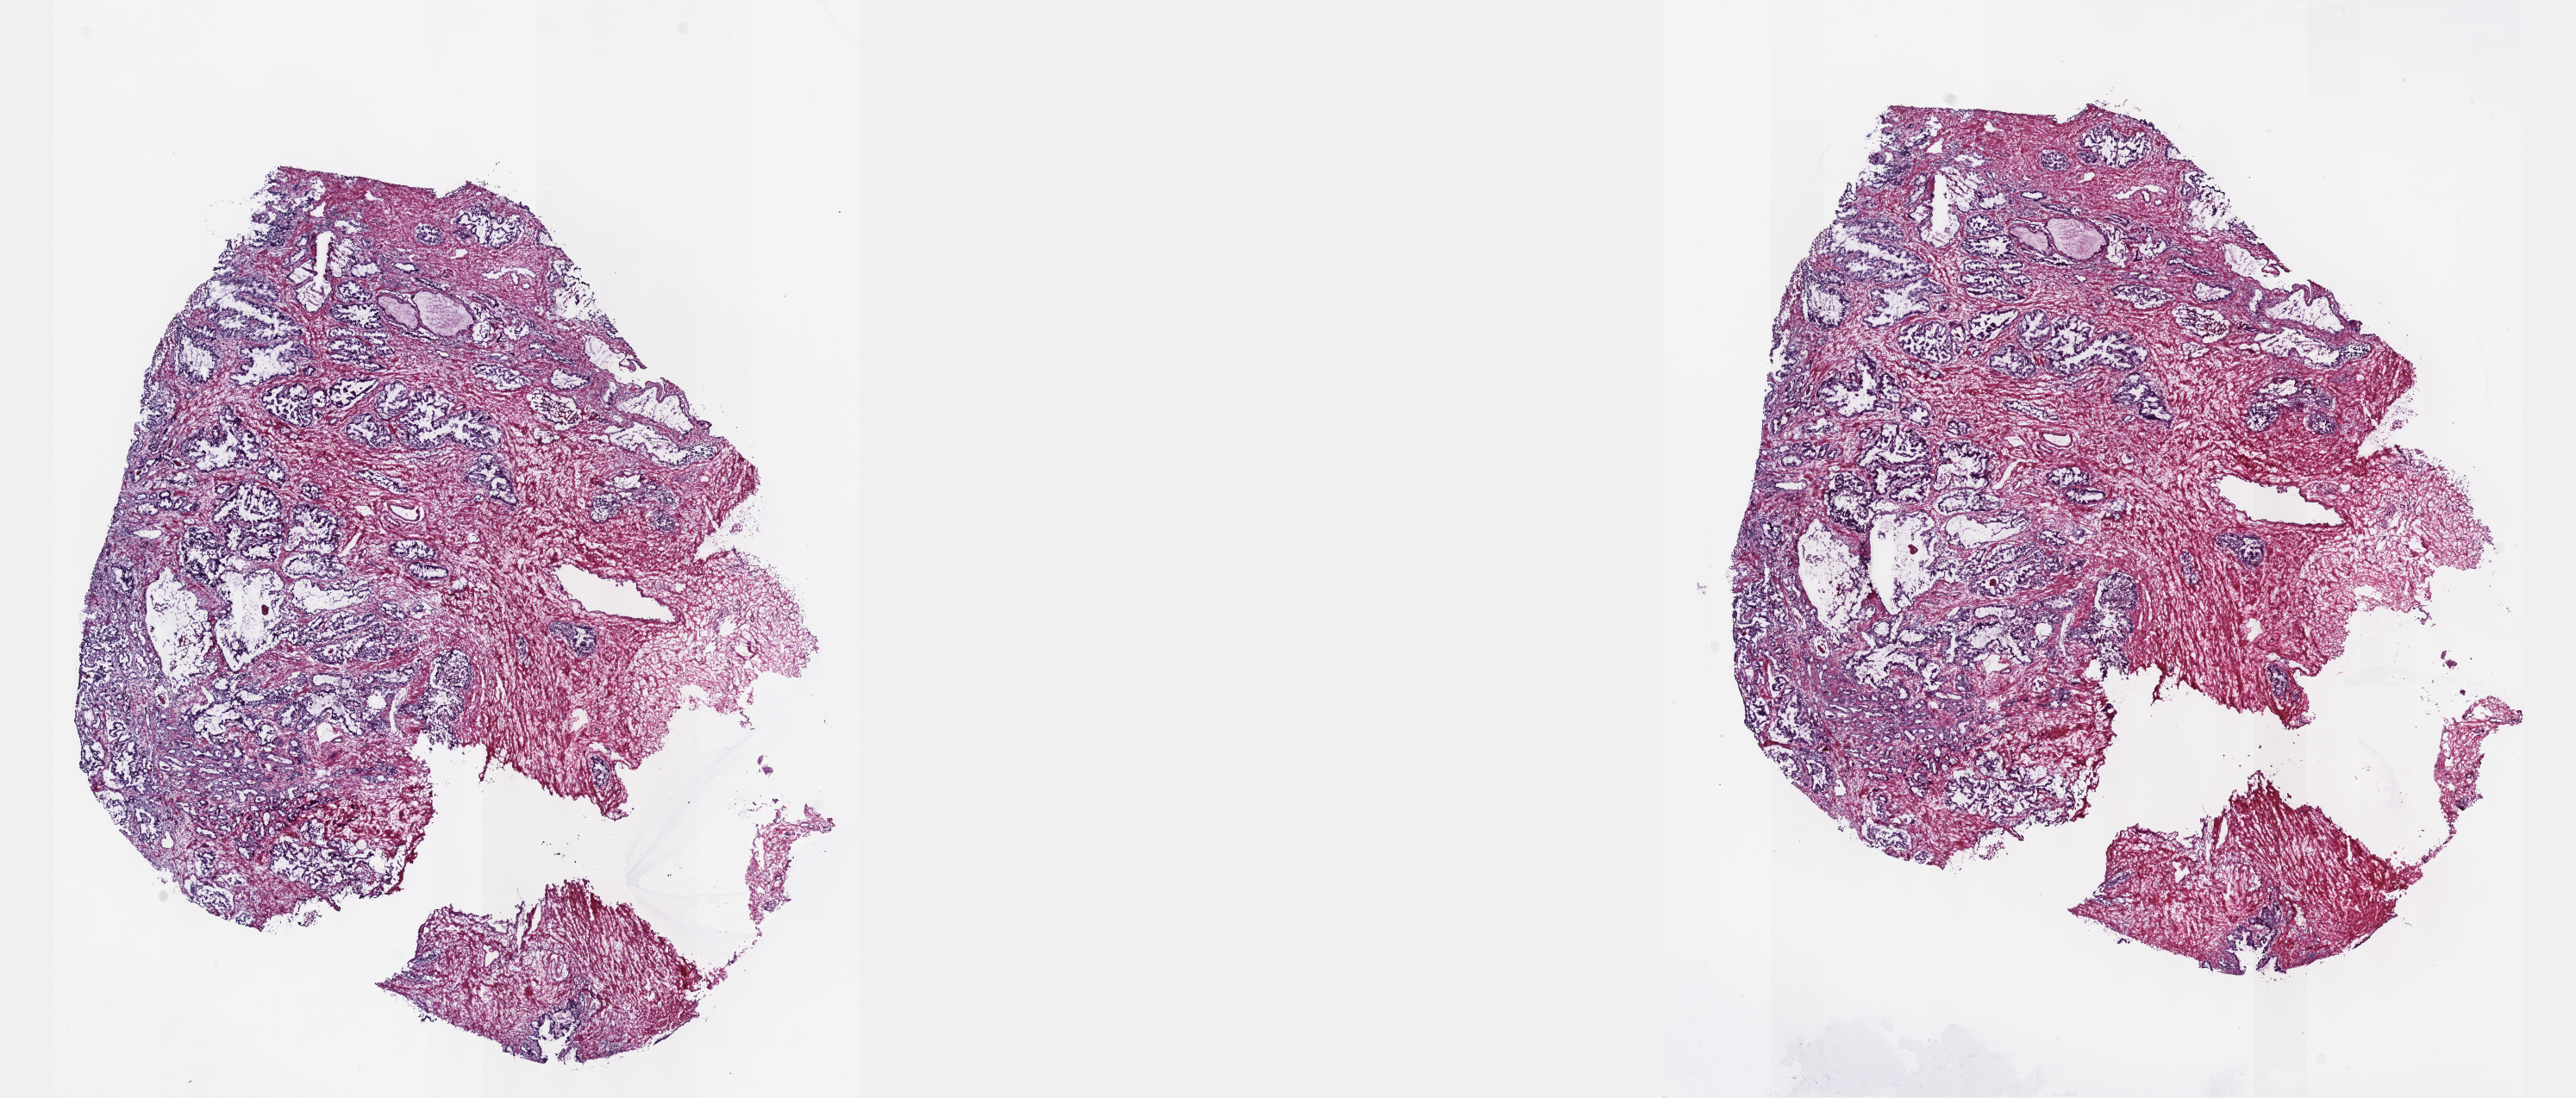
Digitized Hematoxylin and eosin (H&E) stained tissue section (whole slide), shown as a low-resolution overview of the whole scanned area (about 24.1 x 10.3 mm). Frozen section from the top of the tissue portion. Primary tumour sample from the prostate. Patient: male, age at initial diagnosis 71 years. Gleason score: 6 (3+3). Pathologist review of this section (percent, as recorded): tumour cells 30%, tumour nuclei 80%, normal cells 3%, stromal cells 63%, necrosis 4%. Inflammatory infiltration, as recorded: lymphocyte infiltration 8%, monocyte infiltration 1%, neutrophil infiltration 1%.
- laterality: bilateral
- histologic diagnosis: Adenocarcinoma, NOS (prostate gland)